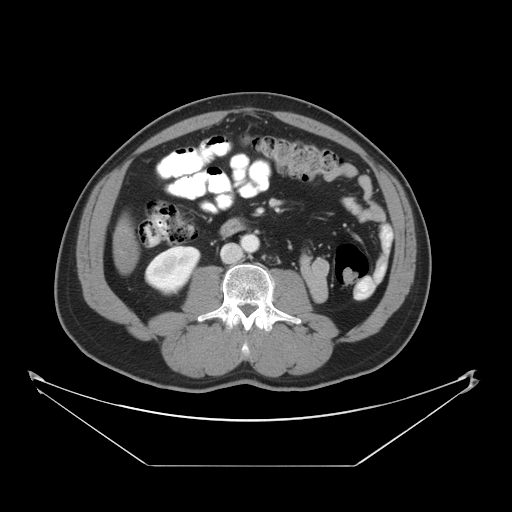
Contrast-enhanced abdominal CT, one axial slice. Intravenous contrast given. Soft-tissue window (W 400 / L 40 HU). 5 mm slice thickness. 512 × 512 image matrix, field of view 465 × 465 mm. Male patient, age 57 years. Case-level facts recorded for this patient, not image findings: diagnosis: colorectal cancer liver metastases, imaged before liver resection; multiple liver metastases: no; largest metastasis: 3.3 cm.
Structures marked on this image (manually delineated by an expert):
- liver: bounding box [x1, y1, x2, y2] px = [116, 224, 136, 271]
- planned liver remnant (the part of the liver to remain after resection): [116, 224, 136, 271]